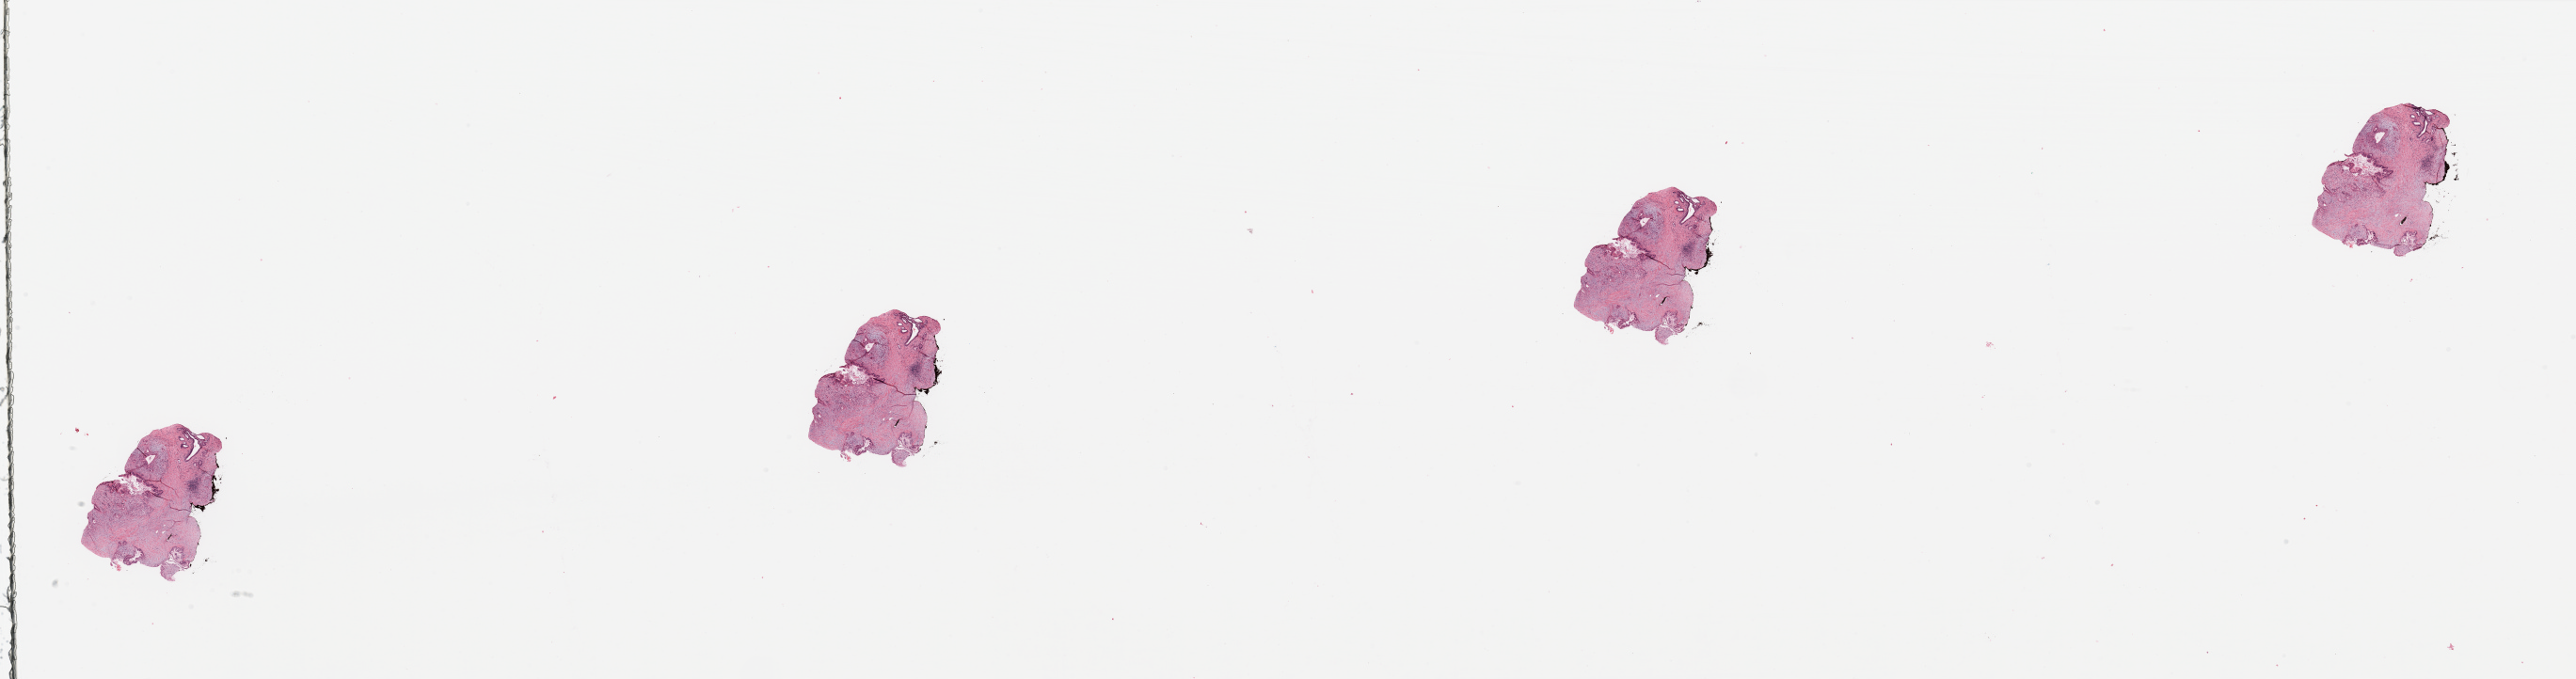
Digitized Hematoxylin and eosin (H&E) stained tissue section (whole slide) — low-resolution overview of the scanned area, about 43.3 x 11.4 mm. Tumour tissue sample, pancreas. Patient: male, age 66 years.
Histologic diagnosis: Infiltrating duct carcinoma, NOS.